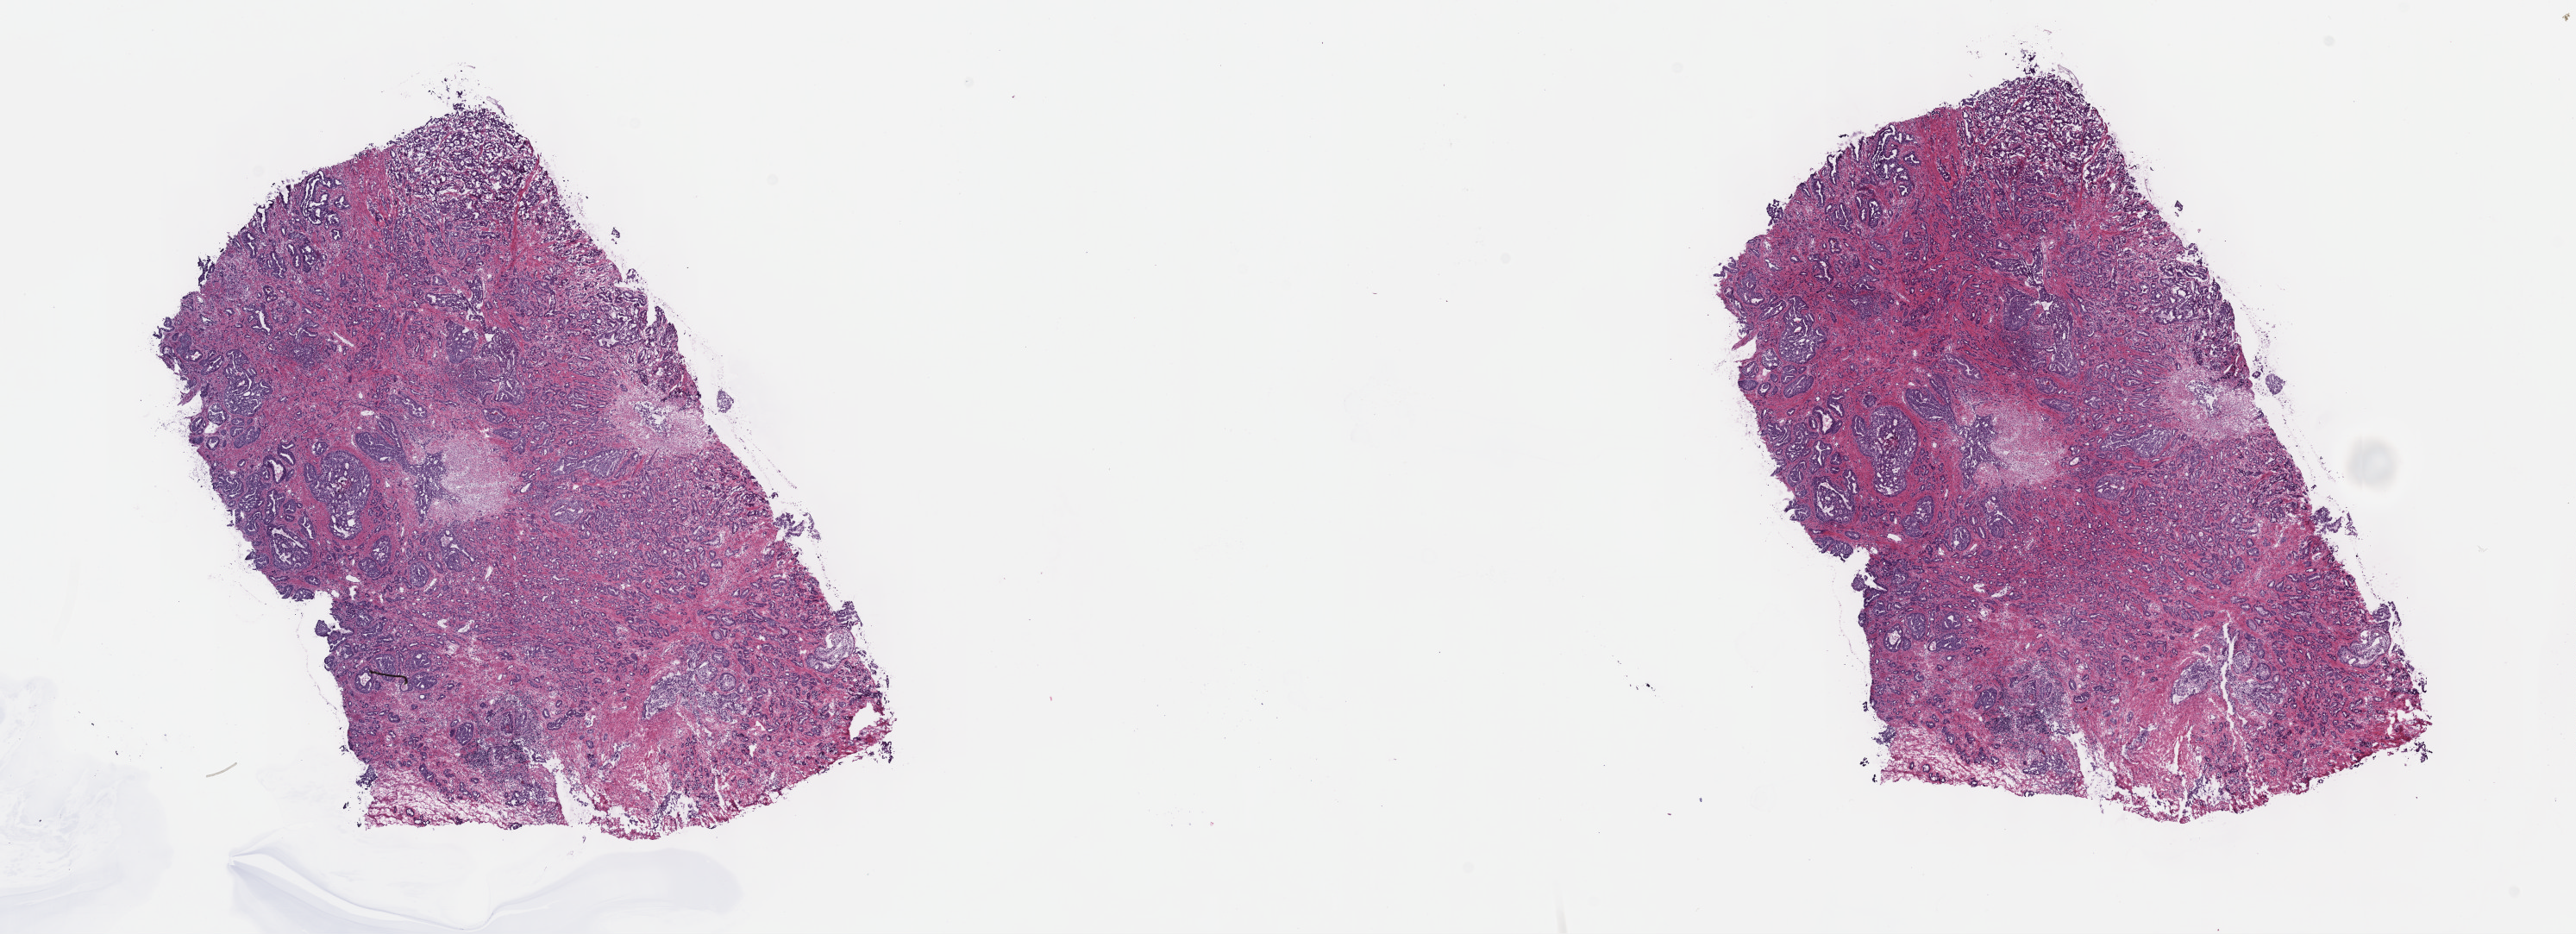
Hematoxylin and eosin (H&E) stained whole-slide image, low-resolution overview of the scanned area, about 24.2 x 8.8 mm (from a 40x scan), frozen section from the top of the tissue portion, primary tumour sample from the prostate. Patient: male, age at initial diagnosis 63 years. Gleason score: 7 (4+3). Slide review estimates, as recorded: tumour cells 65%, tumour nuclei 70%, normal cells 5%, stromal cells 30%, necrosis 0%. Inflammatory infiltration, as recorded: lymphocyte infiltration 0%, monocyte infiltration 0%, neutrophil infiltration 0%.
Laterality: bilateral. Lymph nodes positive (case pathology): 0 of 2 examined. Pathologic diagnosis: Adenocarcinoma, NOS (prostate gland).